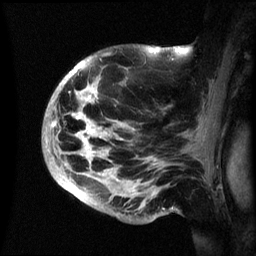
Breast MRI (dynamic contrast-enhanced), one sagittal slice. Position 42 of 60 along the scan axis. Dynamic contrast-enhanced series, image 2 of 3 at this slice position (ordered by acquisition). 1.5 T. TE 4.2 ms, TR 8.4 ms. 2.4 mm slice thickness. 256 × 256 image matrix, field of view 230 × 230 mm. Patient: female, 48 years.
Annotated regions visible in this slice (semi-automatically segmented with operator editing):
- analysis volume of interest (the breast-tissue region the enhancement analysis was run in; not a lesion): bounding box <43,46,192,222> (left, top, right, bottom; pixels)
- tumour enhancement mask (voxels above the 70 % enhancement threshold inside the analysis volume of interest): <59,48,154,192>